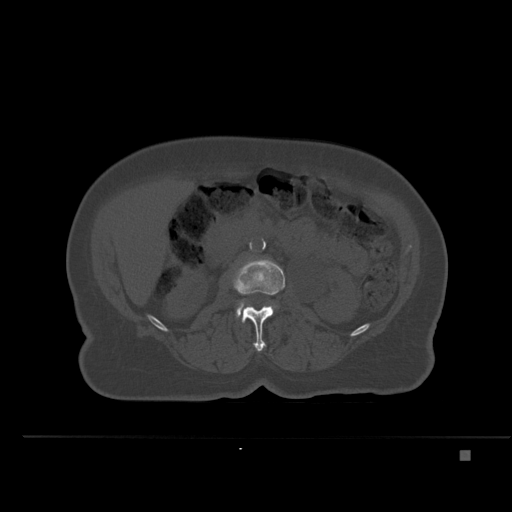
CT including the spine, one axial slice; slice 212 of 477 in the series (ordered by position); bone window (W 1800 / L 400 HU); 1.5 mm slice thickness; 512 × 512 image matrix. Female patient, age 74 years. Case-level facts recorded for this patient, not image findings: primary cancer: colon.
Structures marked on this image (semi-automatic segmentation, software-assisted and operator-edited):
- L2 vertebra: box from (x=232, y=258) to (x=285, y=351) px
- L3 vertebra: (x=236, y=302)–(x=243, y=316)